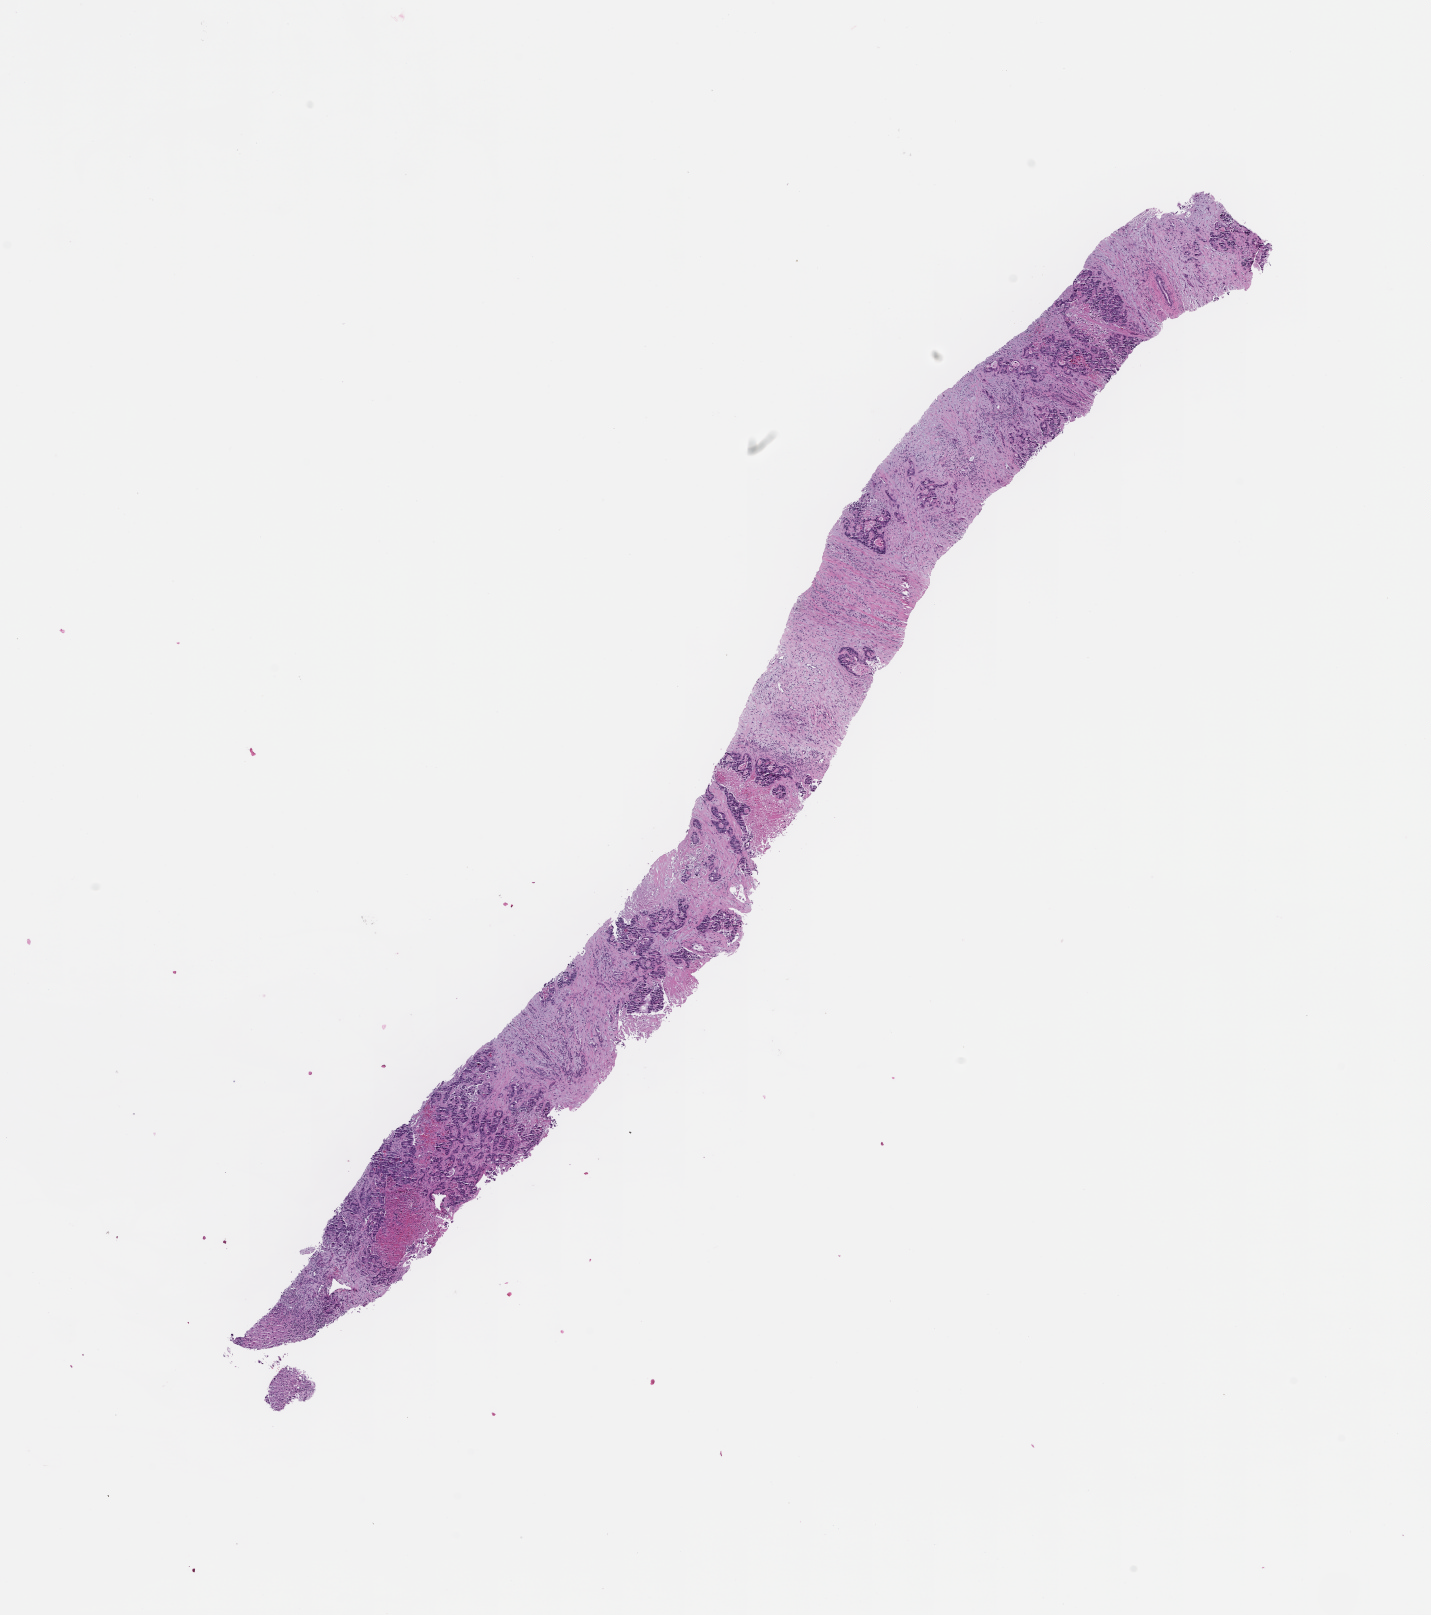
Digitized hematoxylin and eosin (H&E)-stained section, a low-resolution overview of the entire scanned area, about 11.6 x 13.0 mm, FFPE section, collected at disease progression. Patient sex: male.
This section: metastatic tumor tissue. Patient diagnosis (primary): Colorectal Carcinoma.